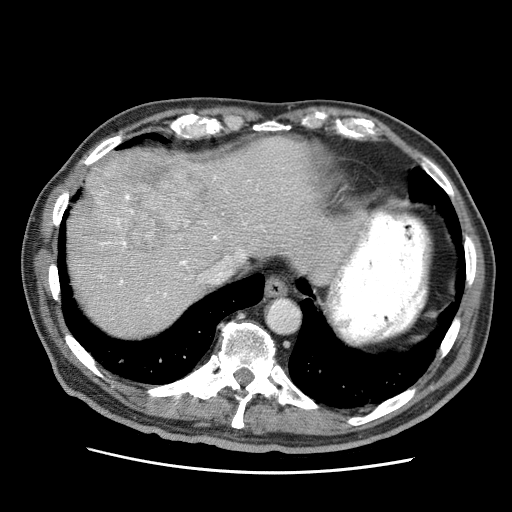
Contrast-enhanced abdominal CT (liver protocol), one axial slice; slice 55 of 75 in the series (ordered by position); reconstruction kernel STANDARD; 120 kVp; soft-tissue window (W 400 / L 40 HU); 512 × 512 image matrix. Case-level facts recorded for this patient, not image findings: diagnosis: hepatocellular carcinoma (patient treated with transarterial chemoembolisation; whether this scan precedes or follows treatment is not stated here); TNM stage (as recorded): Stage-IIIA; Child-Pugh class: A; tumour differentiation: well differentiated.
Structures marked on this image (semi-automatic segmentation, software-assisted and operator-edited):
- liver parenchyma outside the tumour (the mass and vessels are separate outlines, so this box may not span the whole liver): bounding box (x1, y1, x2, y2) in pixels: (68, 136, 330, 336)
- mass: (66, 149, 210, 275)
- liver vessels: (98, 176, 246, 302)